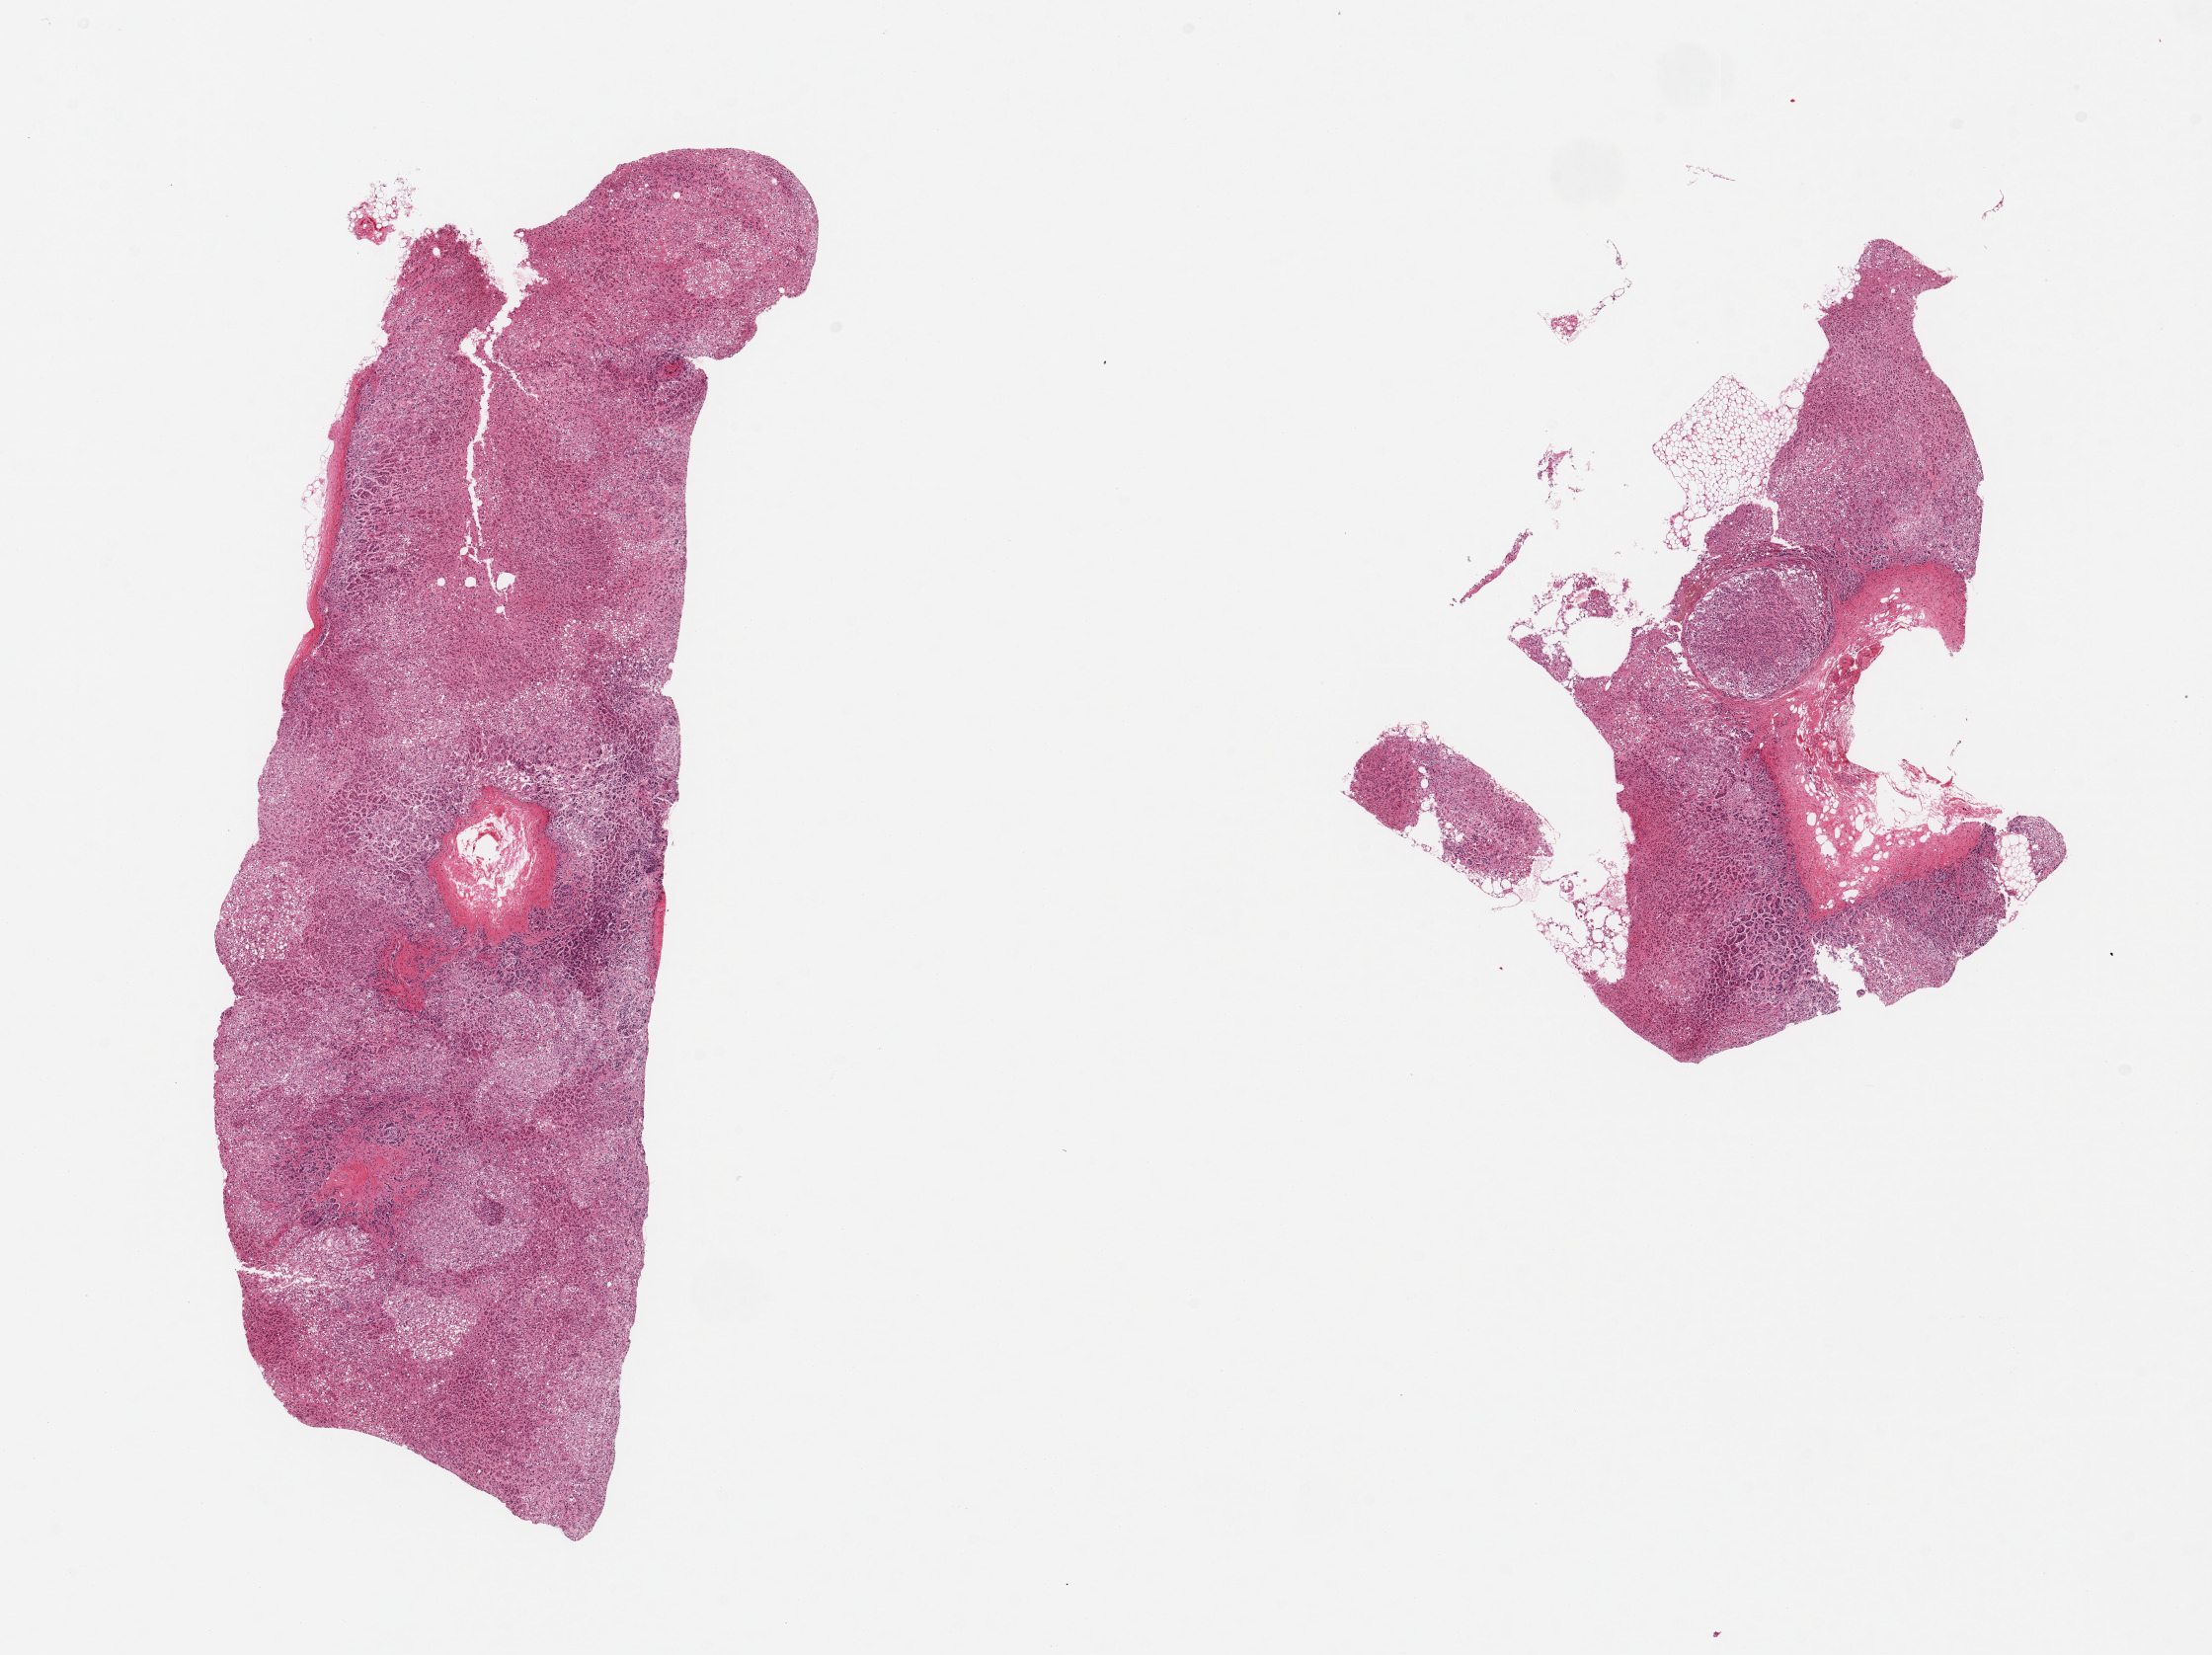
Digitized haematoxylin and eosin-stained section — a low-resolution overview of the entire scanned area, about 17.7 x 13.3 mm (from a 20x scan). PAXgene-fixed paraffin-embedded (PFPE) section. Section of adrenal gland (target tissue). Donor tissue sample.
* reviewer comment on this tissue sample: 2 pieces, cortex, moderately advanced autolysis